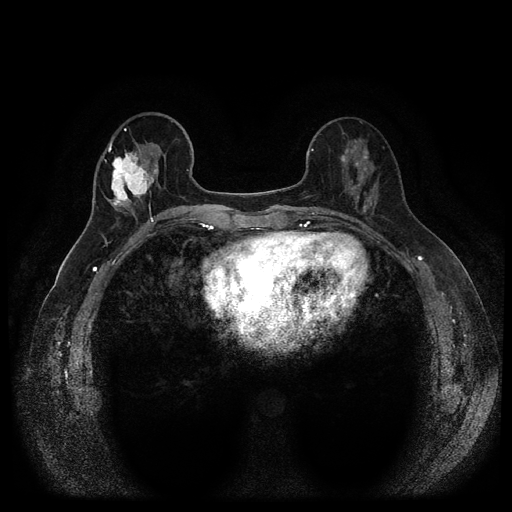
Breast MRI (dynamic contrast-enhanced, multi-phase), one axial slice. Slice 40 of 116 in the series (ordered by position). Dynamic contrast-enhanced series, time point 2 of 5 at this slice position (early post-contrast). 1.5 T. TE 2.6 ms, TR 5.4 ms. 2 mm slice thickness. 512 × 512 image matrix, field of view 340 × 340 mm. Female patient, age 56 years.
Outlined on this slice (semi-automatically segmented with operator editing):
- breast lesion (labelled 'tumour' in the annotation; benign lesions carry a separate 'benign' label): bounding box [x1, y1, x2, y2] px = [108, 147, 166, 209]